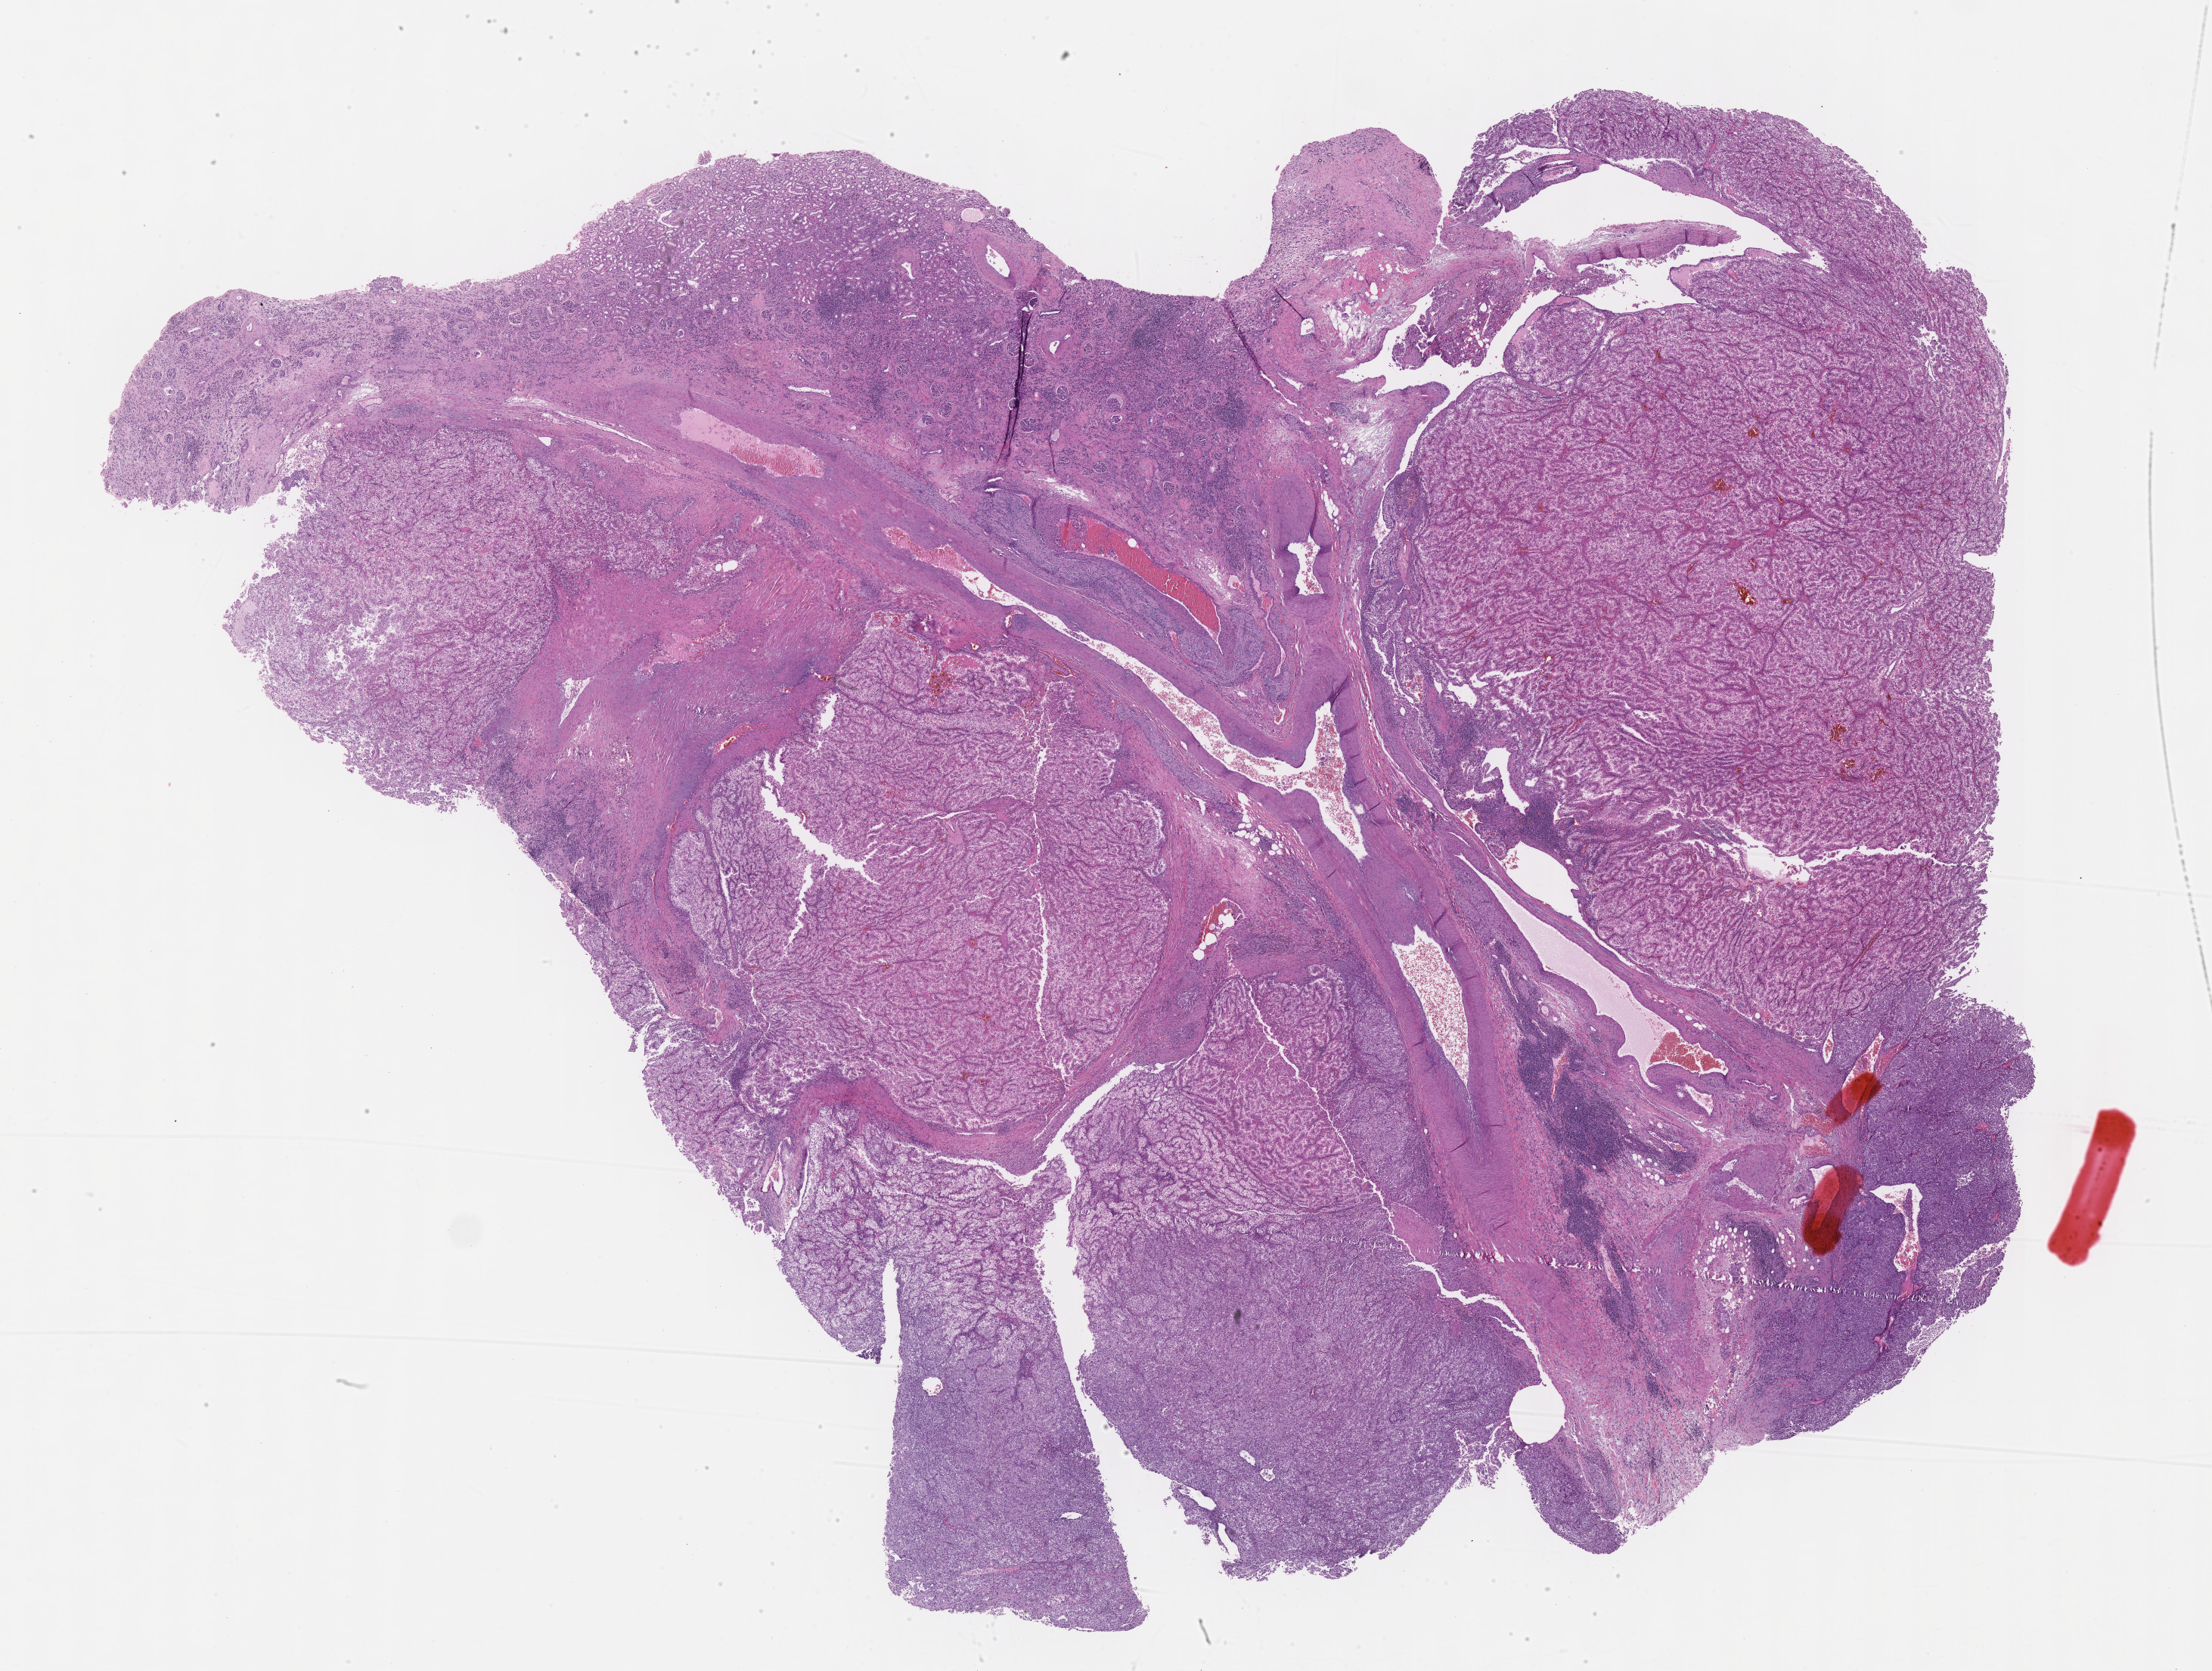
Digitized H&E tissue section (whole slide), whole scanned area (about 23.6 x 17.9 mm) shown as a low-resolution overview, formalin-fixed paraffin-embedded (FFPE) diagnostic section, primary tumour sample from the kidney. Female patient; age at initial diagnosis 55 years. Histologic grade: G4 (undifferentiated).
Laterality: left. Diagnosis: Clear cell adenocarcinoma, NOS. AJCC pathologic stage: IV.